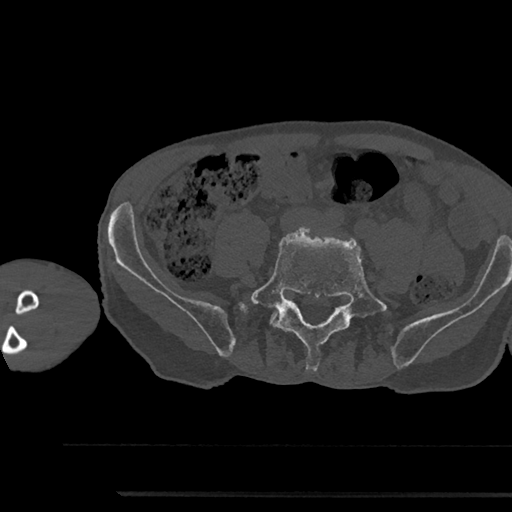
CT including the spine, one axial slice; position 349 of 797 along the scan axis; 120 kVp; bone window (W 1800 / L 400 HU); 0.5 mm slice thickness; 512 × 512 image matrix, field of view 367 × 367 mm. Patient: male, 79 years. Case-level facts recorded for this patient, not image findings: primary cancer: prostate.
Outlined on this slice (semi-automatically segmented with operator editing):
- L5 vertebra: box from (x=244, y=227) to (x=391, y=370) px